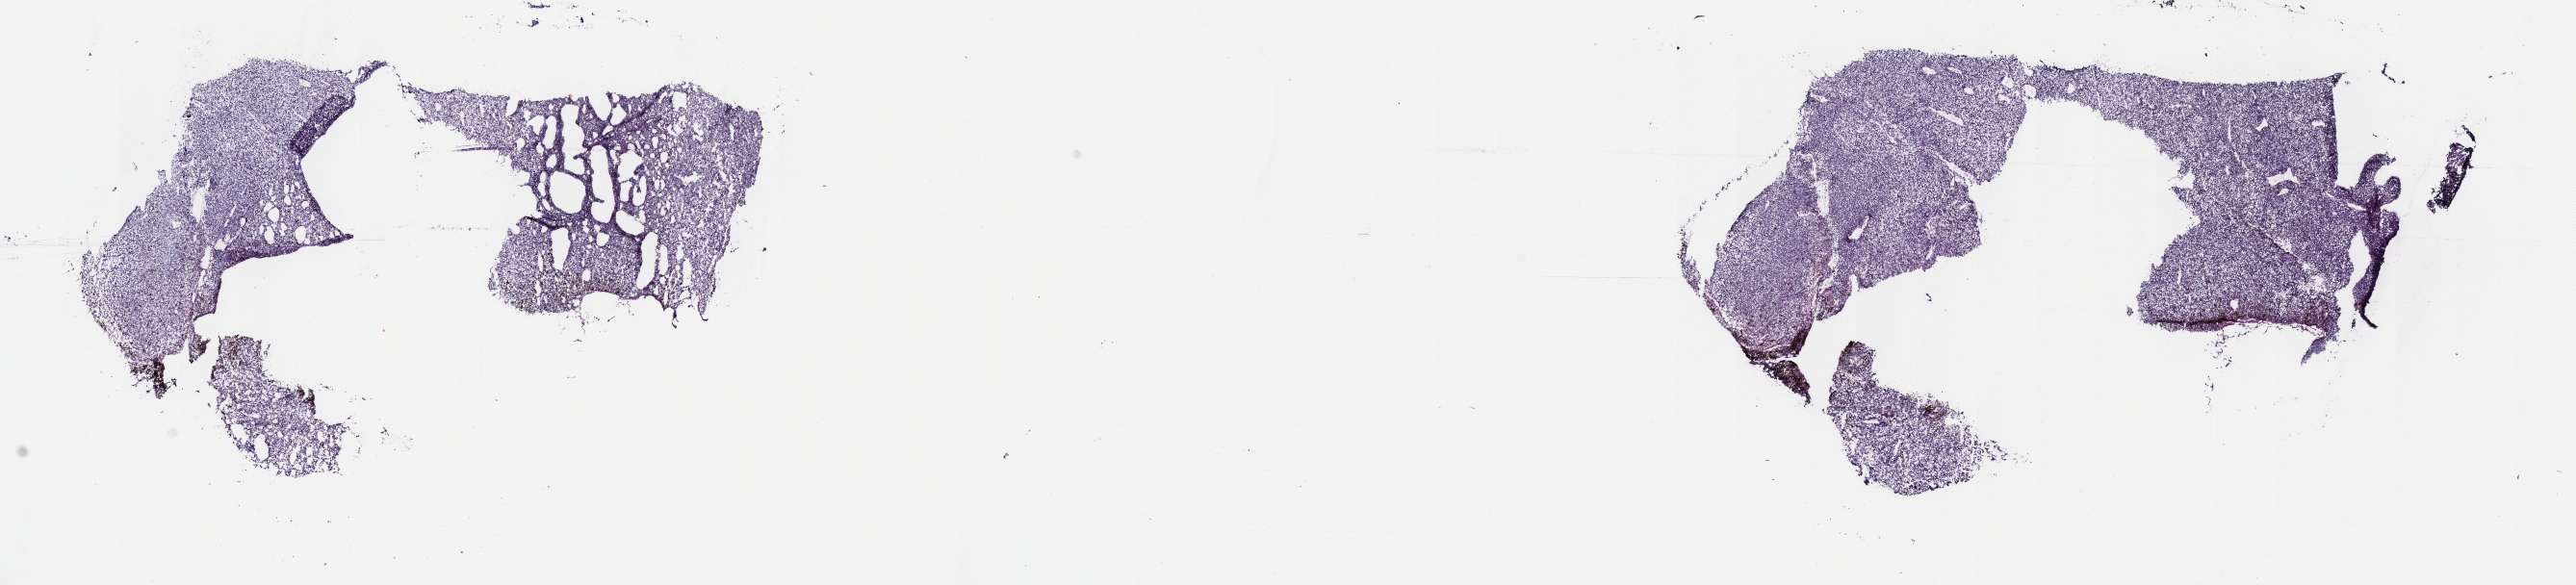
Digitized Hematoxylin and eosin (H&E) stained tissue section (whole slide), a low-resolution overview of the entire scanned area, about 21.6 x 4.9 mm (acquisition: 40x scan), frozen section, primary tumour sample from the uvea. Male patient; age at initial diagnosis 41 years. Pathologist review of this section (percent, as recorded): tumour cells 98%, tumour nuclei 88%, normal cells 0%, stromal cells 0%, necrosis 2%. Inflammatory infiltration, as recorded: lymphocyte infiltration 10%, monocyte infiltration 0%, neutrophil infiltration 0%.
• AJCC pathologic stage: IIIA (7th edition)
• laterality: right
• histologic diagnosis: Mixed epithelioid and spindle cell melanoma (choroid)
• TNM: T4a N0 M0